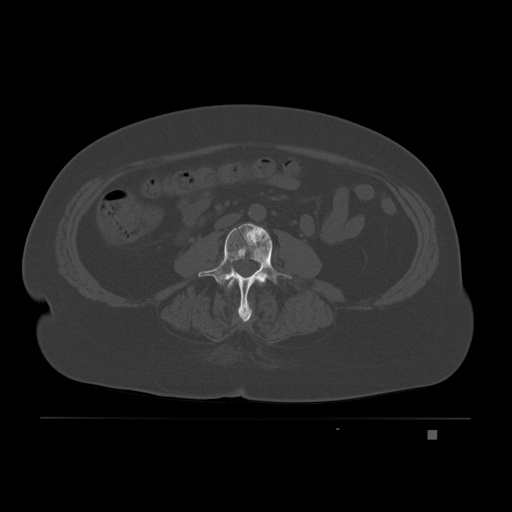
CT including the spine, one axial slice. Position 51 of 221 along the scan axis. Bone window (W 1800 / L 400 HU). 512 × 512 image matrix, field of view 474 × 474 mm. Female patient, age 63 years. Case-level facts recorded for this patient, not image findings: primary cancer: breast.
Outlined on this slice (semi-automatically segmented with operator editing):
- L2 vertebra: bounding box [x1, y1, x2, y2] px = [227, 278, 262, 289]
- L3 vertebra: [198, 223, 292, 322]